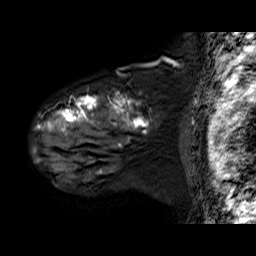
Breast MRI (dynamic contrast-enhanced), one sagittal slice; position 50 of 60 along the scan axis; dynamic contrast-enhanced series, time point 2 of 6 at this slice position (early post-contrast); 1.5 T; TE 6.3 ms, TR 32.9 ms; 256 × 256 image matrix, field of view 200 × 200 mm. Female patient. From the clinical record (not read from this slice): setting: breast cancer imaged before/during neoadjuvant chemotherapy; receptor status: HER2-positive.
Structures marked on this image (semi-automatic segmentation, software-assisted and operator-edited):
- analysis volume of interest (the breast-tissue region the enhancement analysis was run in; not a lesion): bounding box <32,87,182,180> (left, top, right, bottom; pixels)
- tumour enhancement mask (voxels above the 100 % enhancement threshold inside the analysis volume of interest): <34,93,150,174>